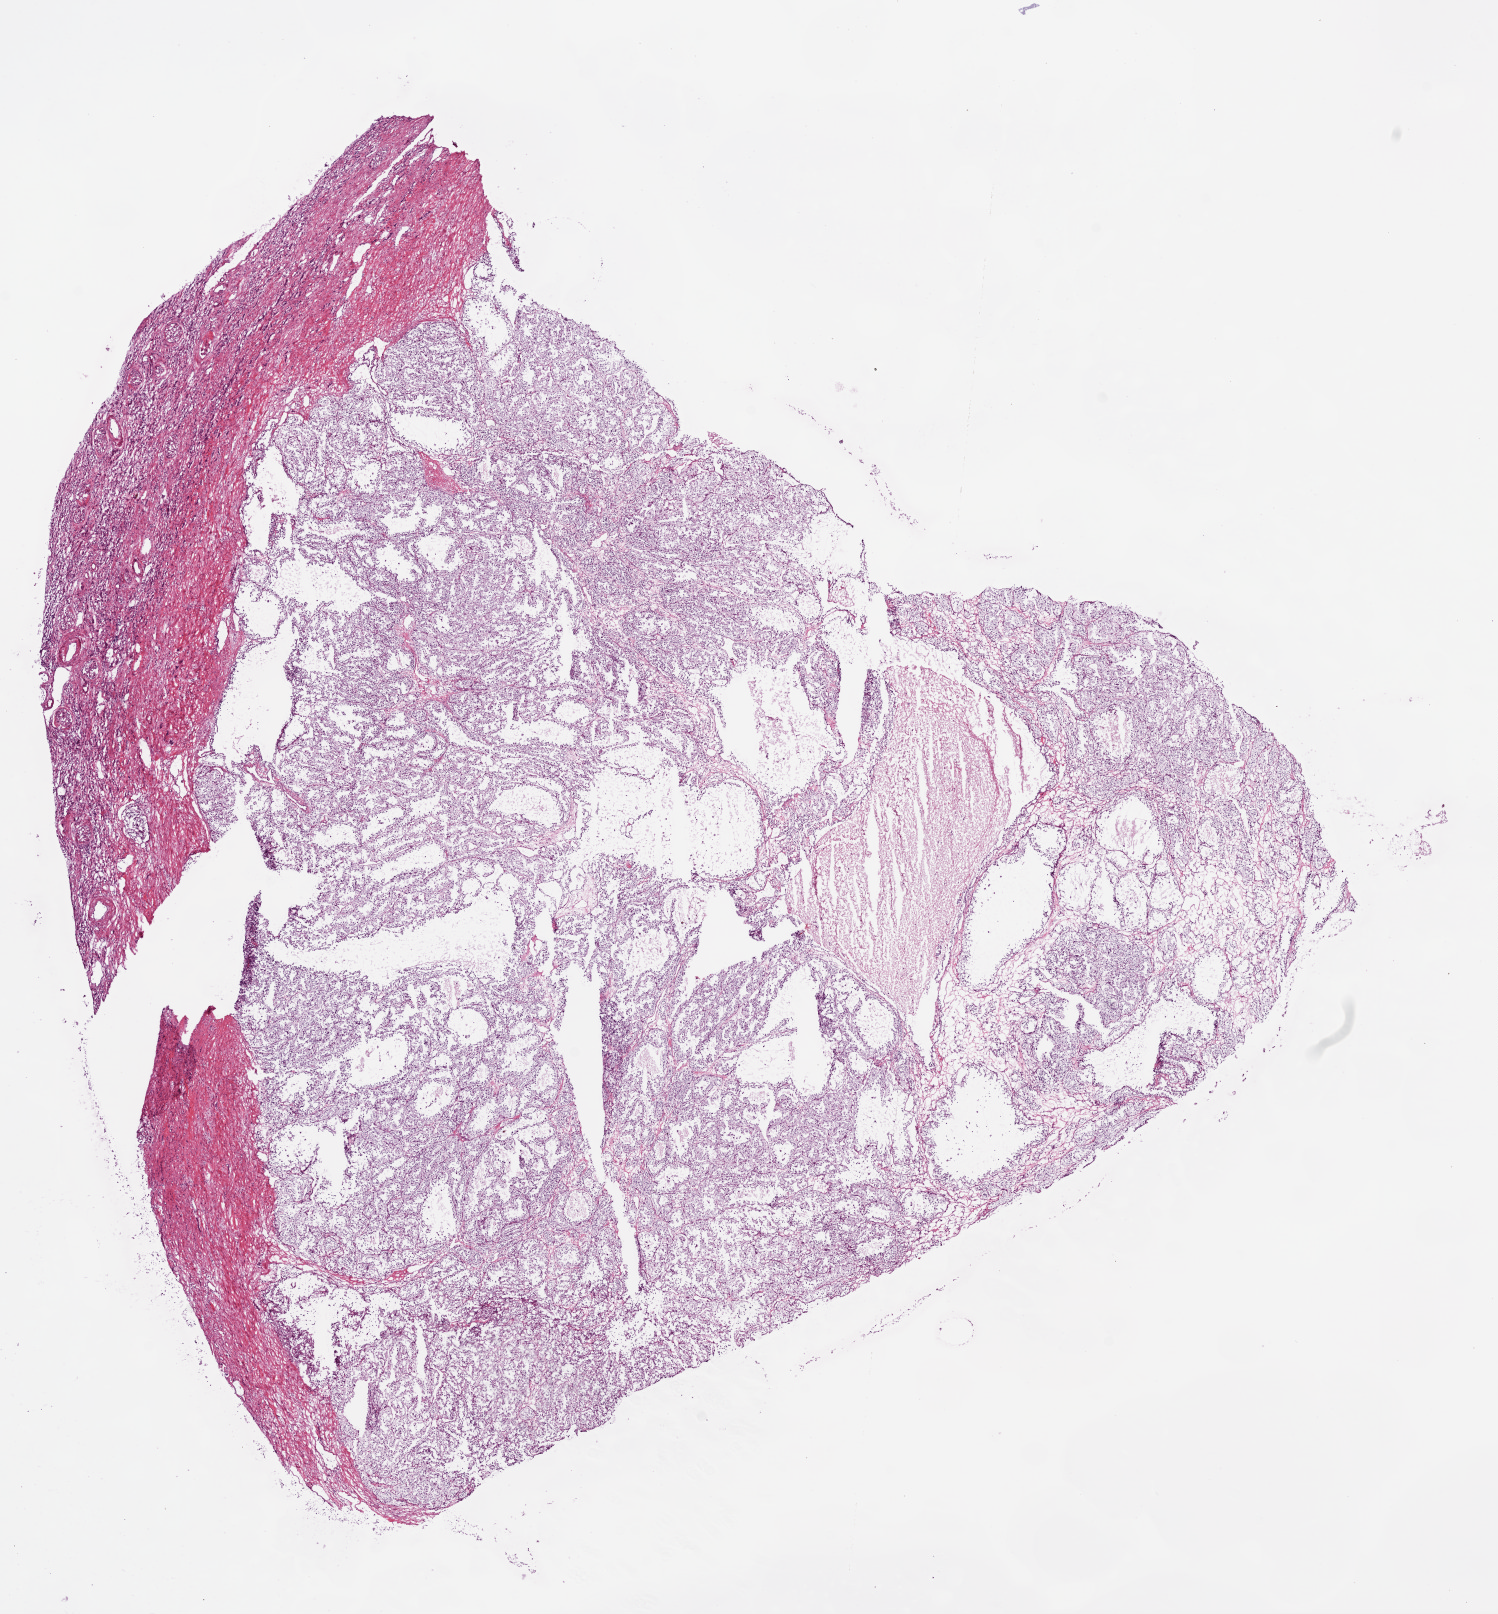
Digitized H&E-stained tissue section (whole slide), shown as a low-resolution overview of the whole scanned area (about 12.1 x 13.0 mm); frozen section from the bottom of the tissue portion; sample: primary tumour, kidney. Male patient; age at initial diagnosis 45 years. Histologic grade: G2 (moderately differentiated). Composition of this section per pathologist review: tumour cells 80%, tumour nuclei 80%, normal cells 20%, stromal cells 0%, necrosis 0%. Infiltration values recorded for this section: lymphocyte infiltration 0%, monocyte infiltration 0%, neutrophil infiltration 0%.
- laterality: right
- AJCC pathologic stage: I
- diagnosis: Clear cell adenocarcinoma, NOS